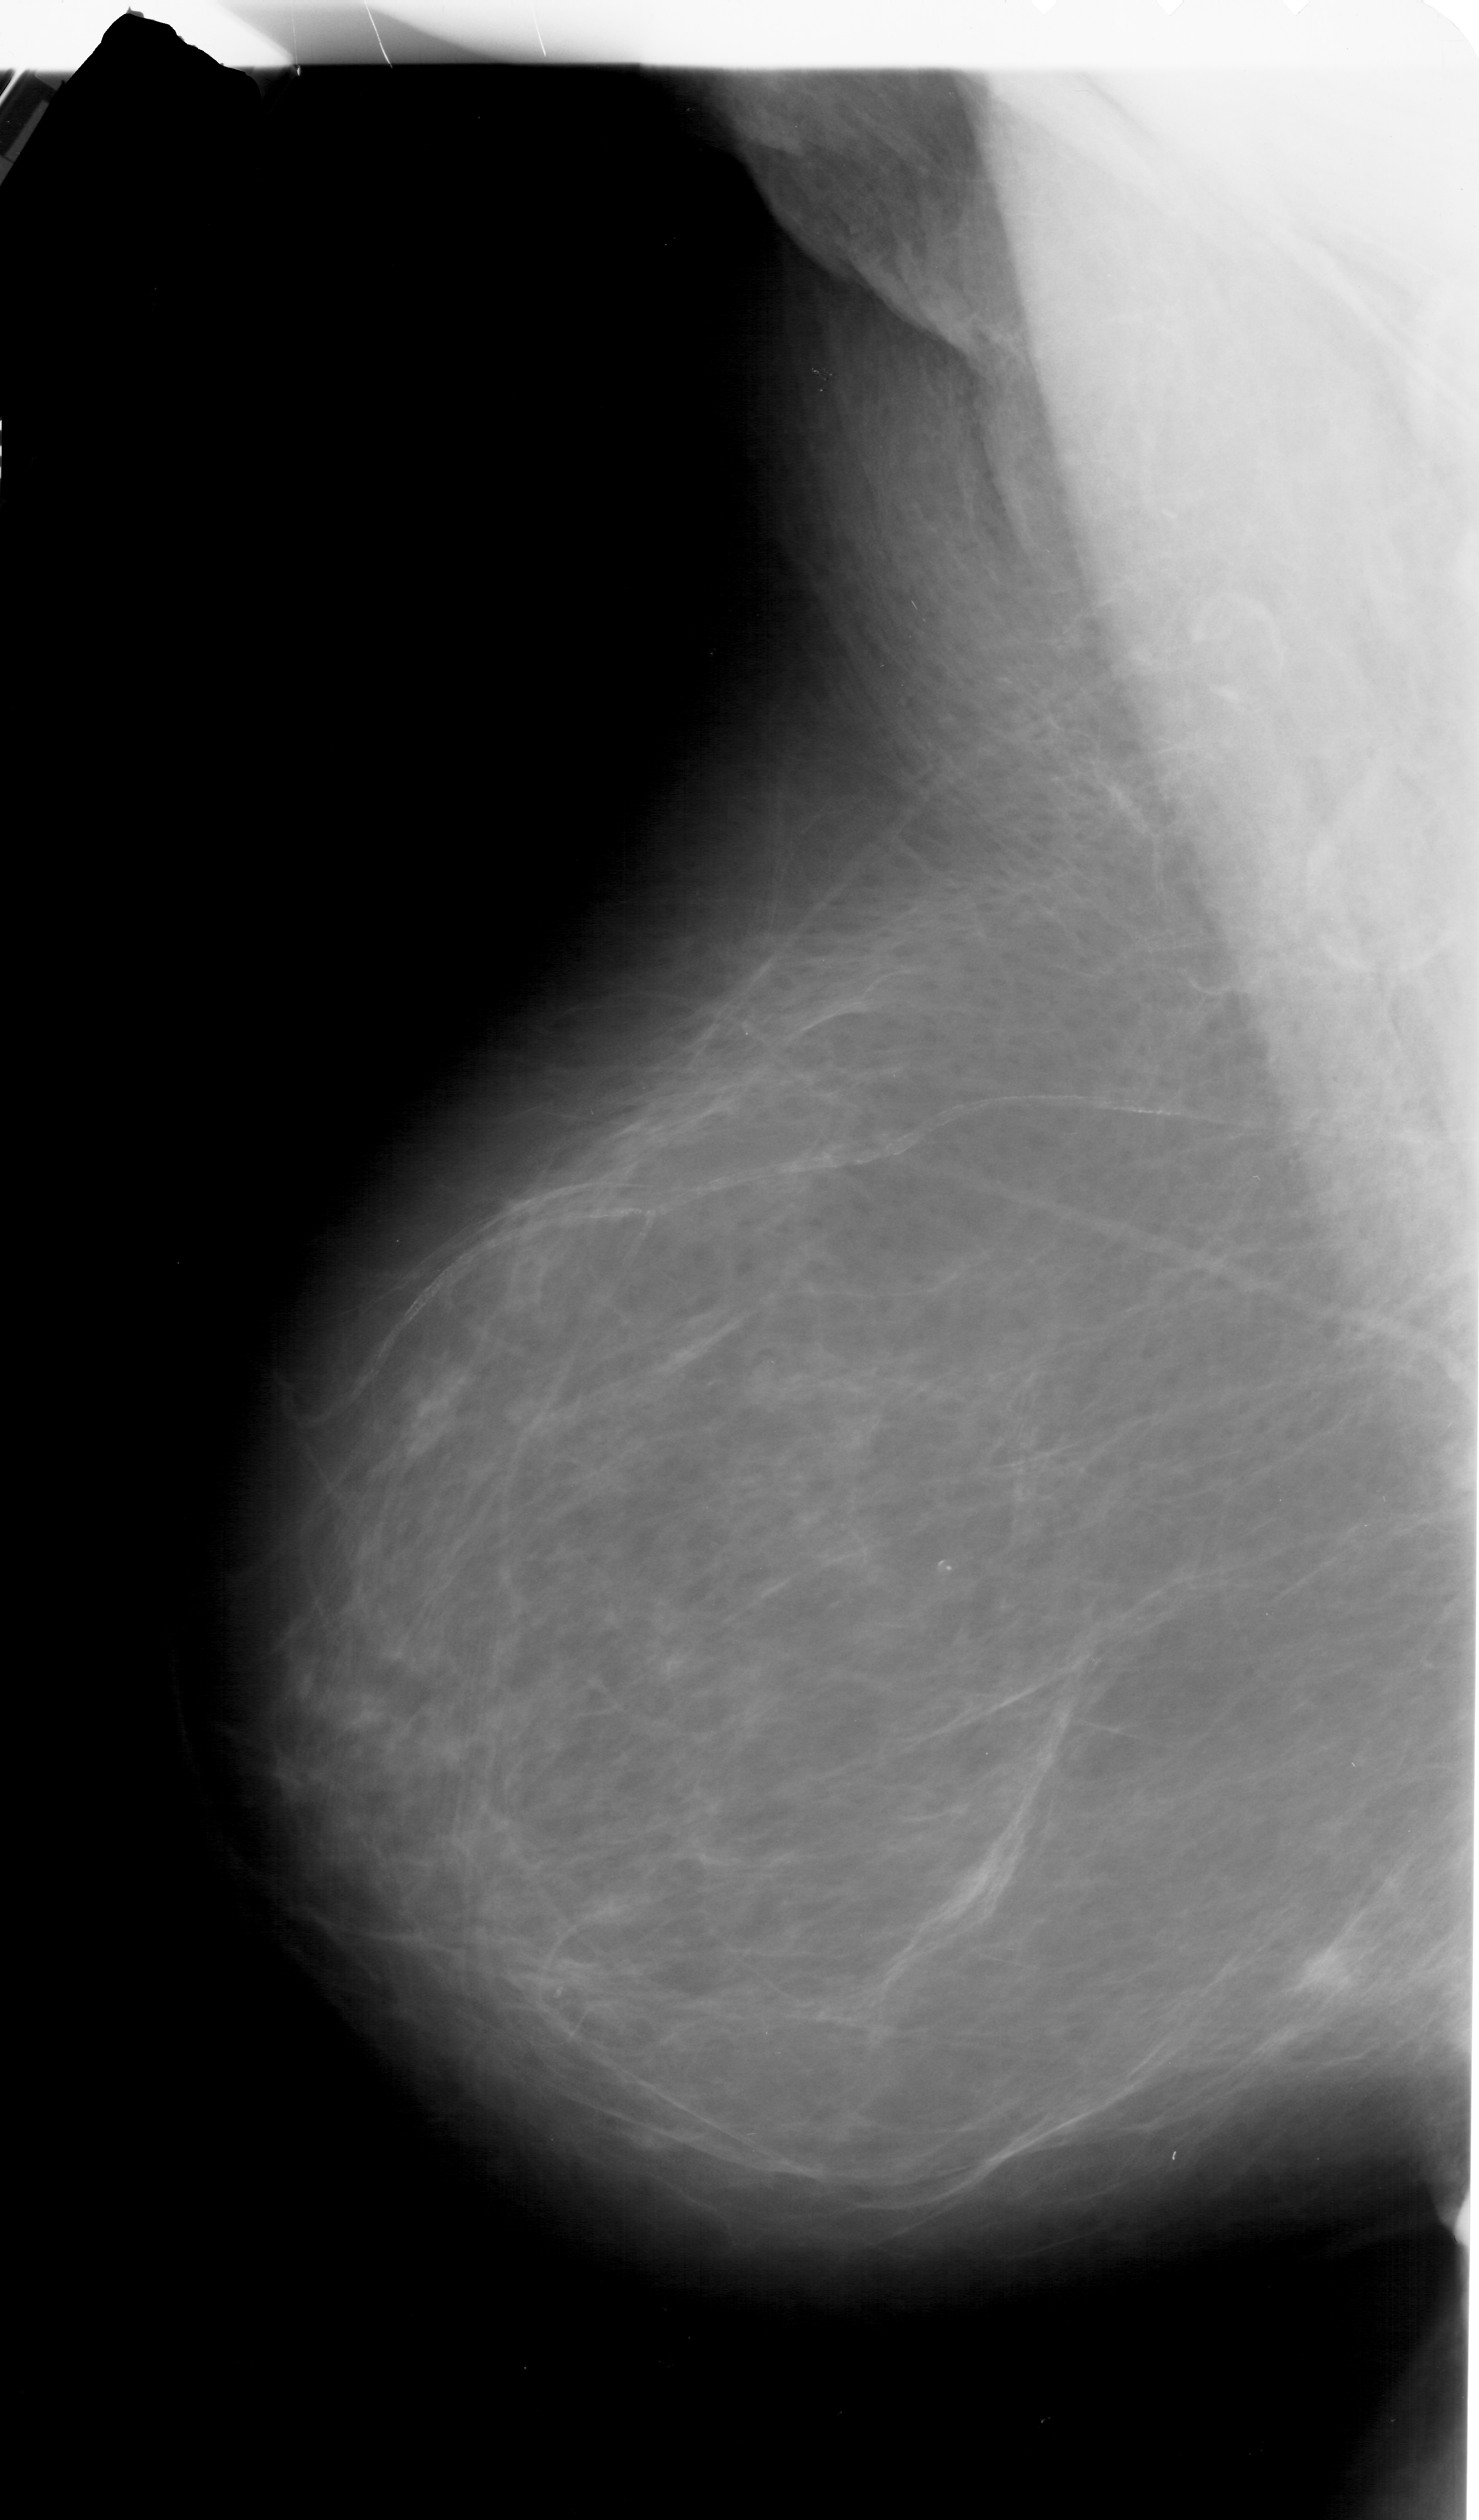
Scanned film-screen mammogram; left breast; MLO view; breast composition: scattered fibroglandular densities (BI-RADS density category 2 of 4).
Finding: mass, shape irregular, margins ill defined; BI-RADS assessment category 4; pathology (as recorded): malignant.